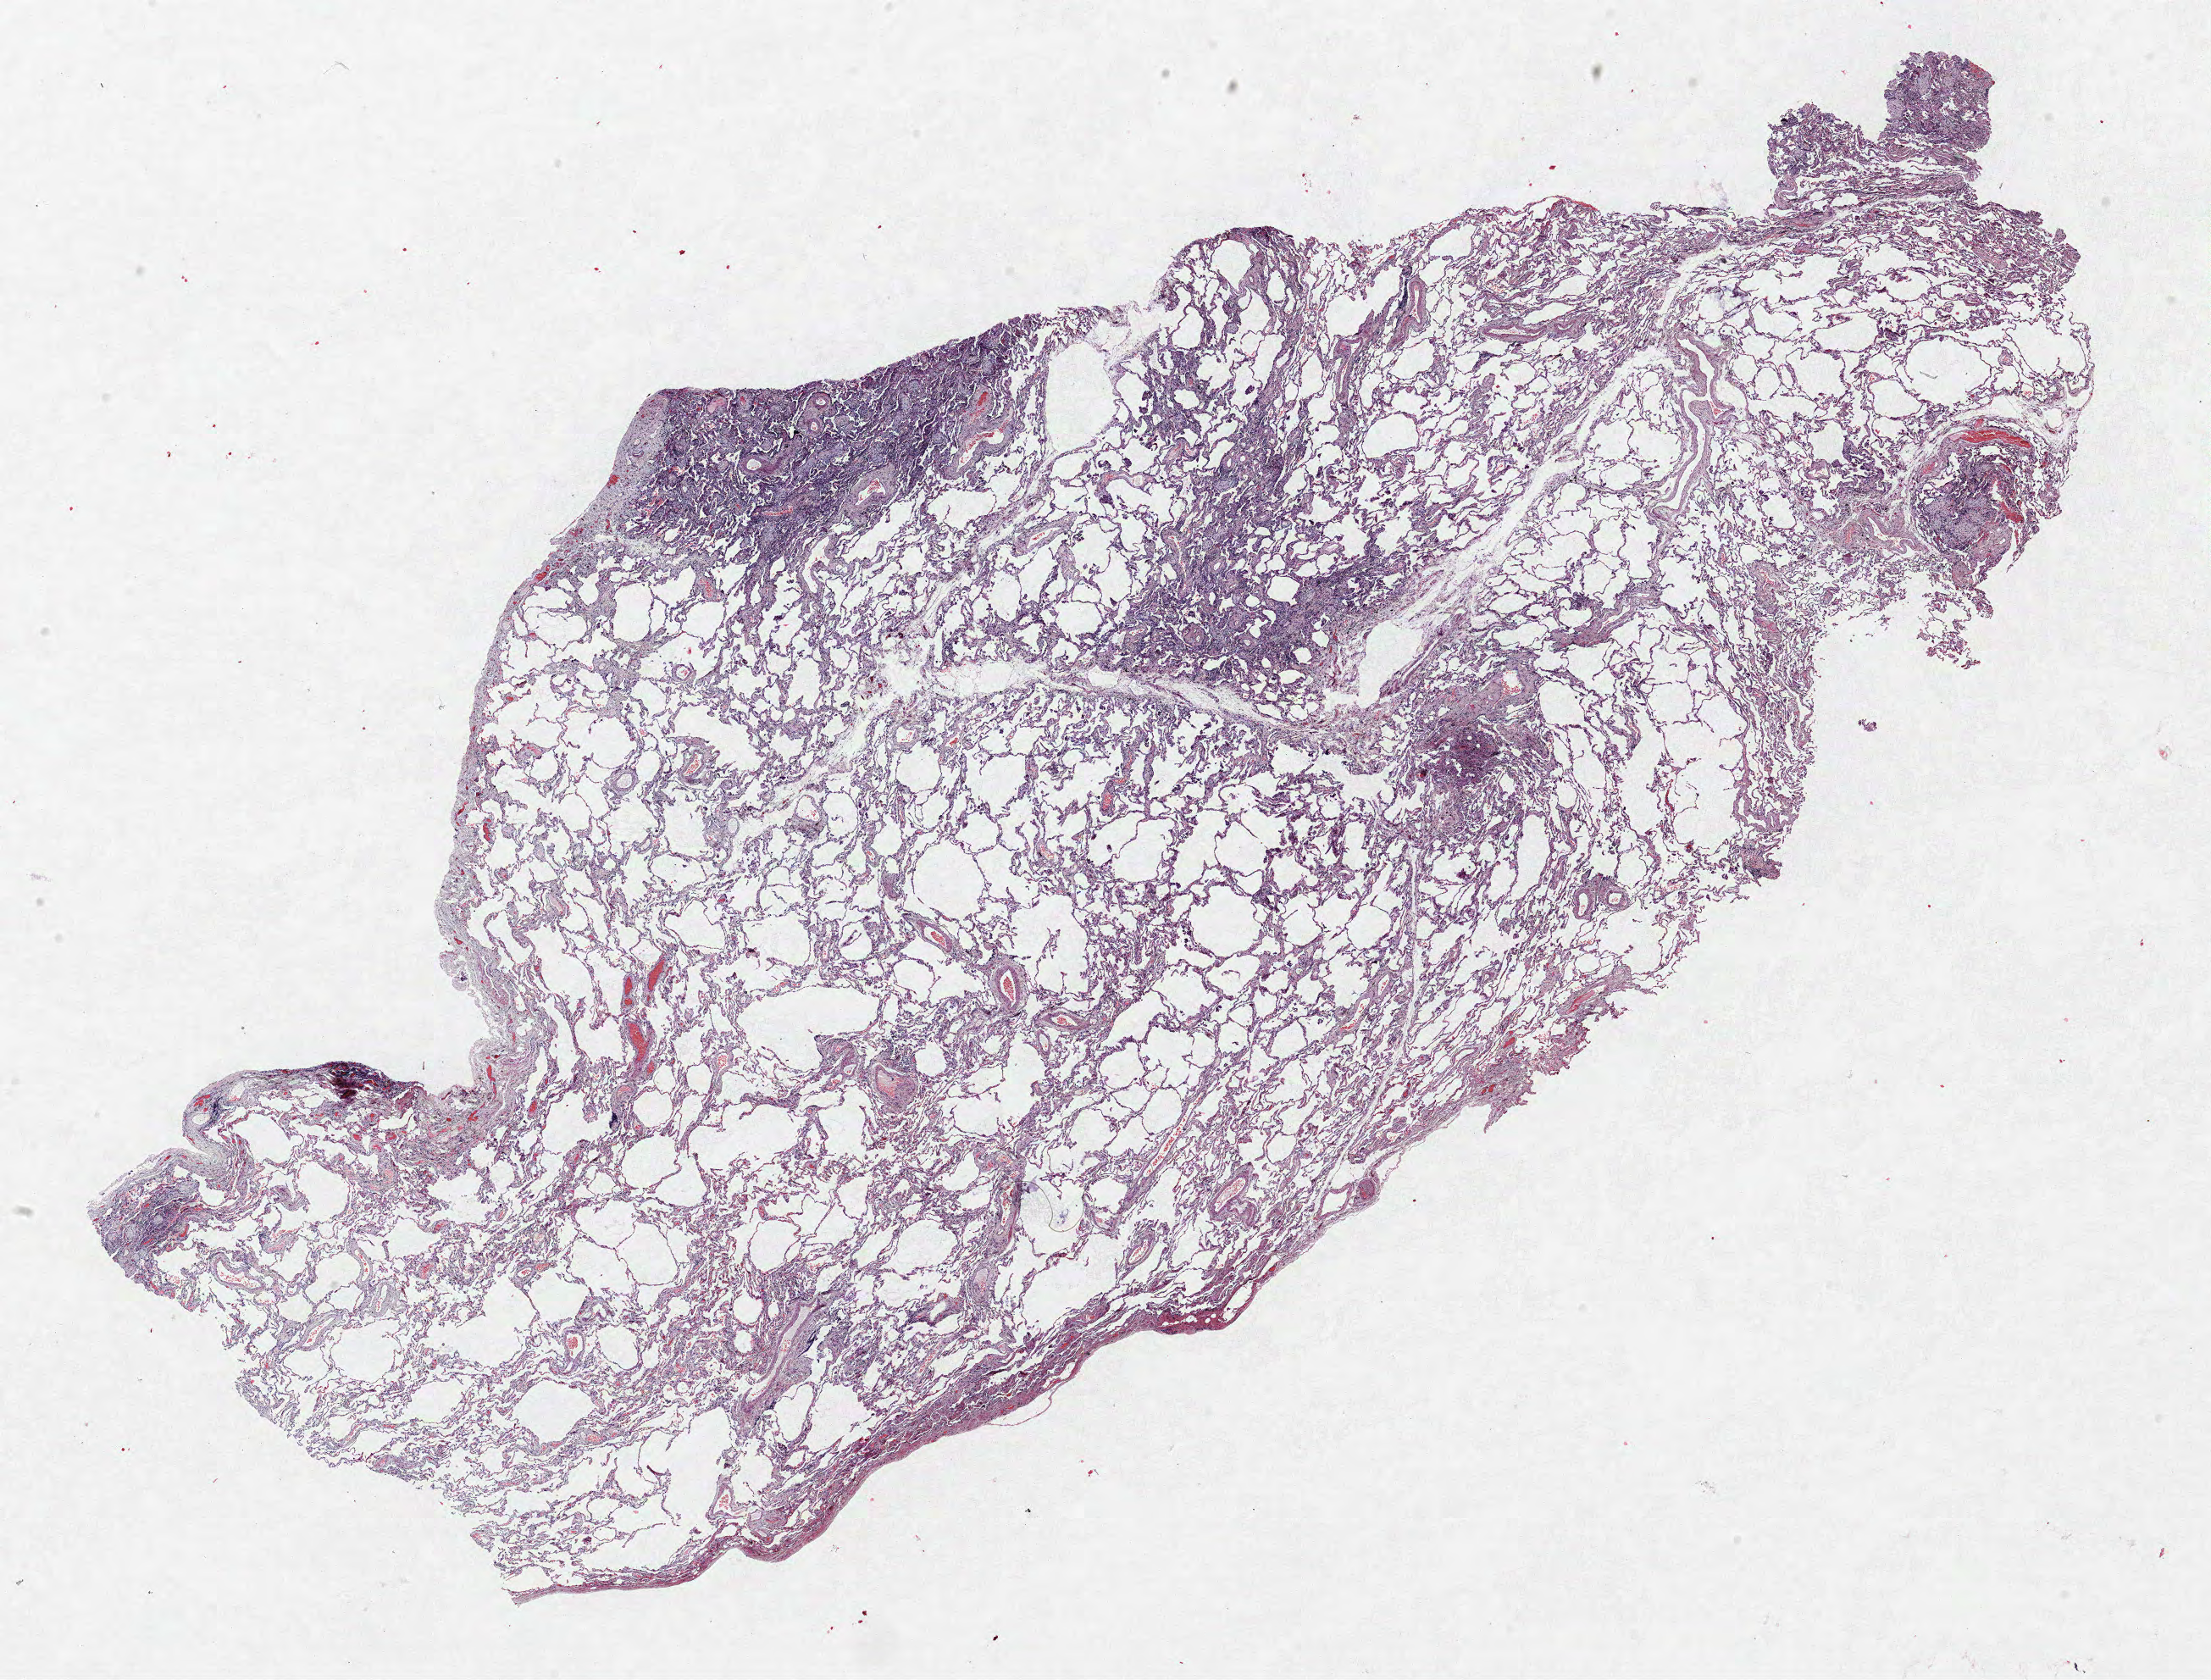
Whole-slide histology image, H&E — shown as a low-resolution overview of the whole scanned area (about 20.9 x 15.9 mm); FFPE section; lung. Female patient, aged 70 at enrolment.
Participant's lung-cancer diagnosis: Clear cell adenocarcinoma, NOS.